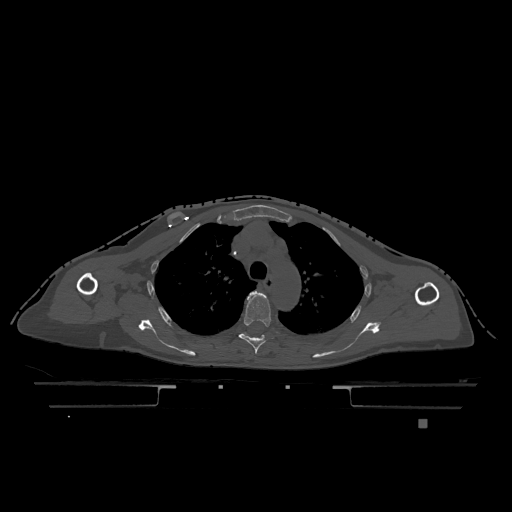
CT including the spine, one axial slice; position 878 of 1317 along the scan axis; bone window (W 1800 / L 400 HU); 0.5 mm slice thickness; 512 × 512 image matrix. Patient: female, 74 years. From the clinical record (not read from this slice): primary cancer: lung.
Annotated regions visible in this slice (semi-automatic segmentation, software-assisted and operator-edited):
- T4 vertebra: bounding box (x1, y1, x2, y2) in pixels: (238, 291, 274, 354)